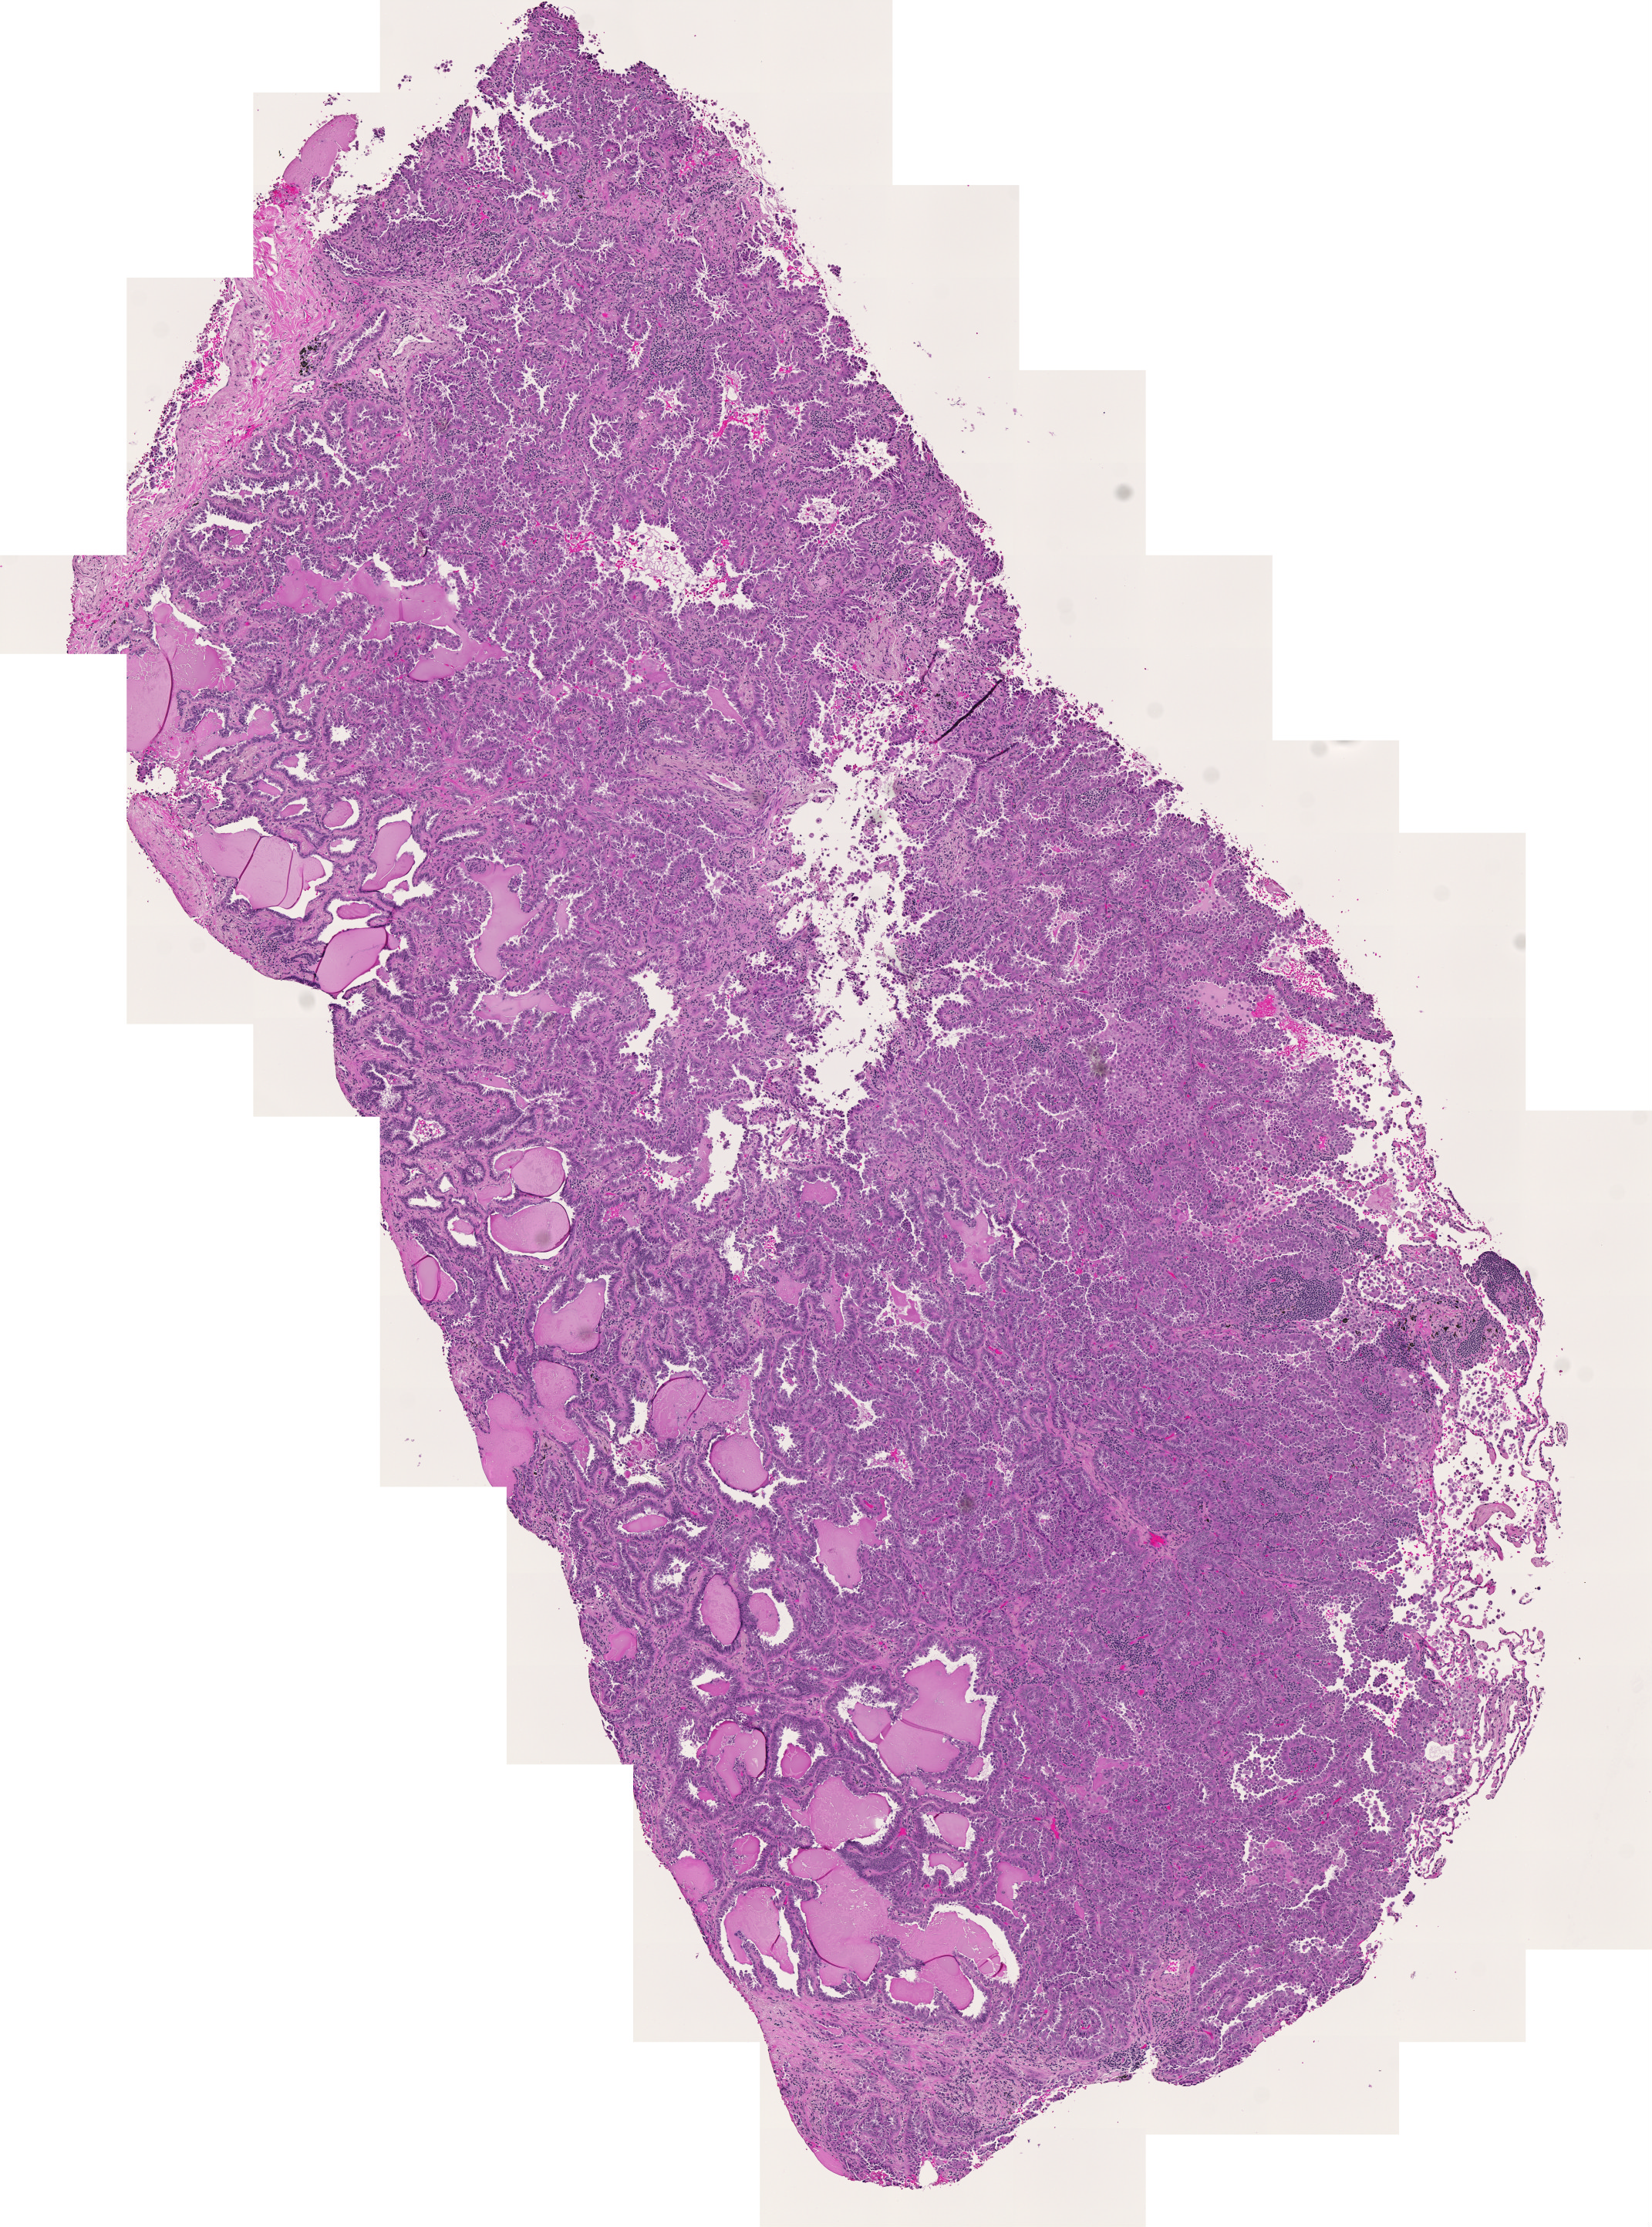
Digitized Hematoxylin and eosin (H&E) stained tissue section (whole slide) — shown as a low-resolution overview of the whole scanned area (about 5.5 x 7.5 mm), tumour tissue sample, sampled site: lung. Male, 73 y/o. Histologic grade: G1 (well differentiated). Slide review estimates, as recorded: tumour nuclei 80%, necrosis 3%.
Diagnosis: Adenocarcinoma, NOS. AJCC pathologic stage: IA.